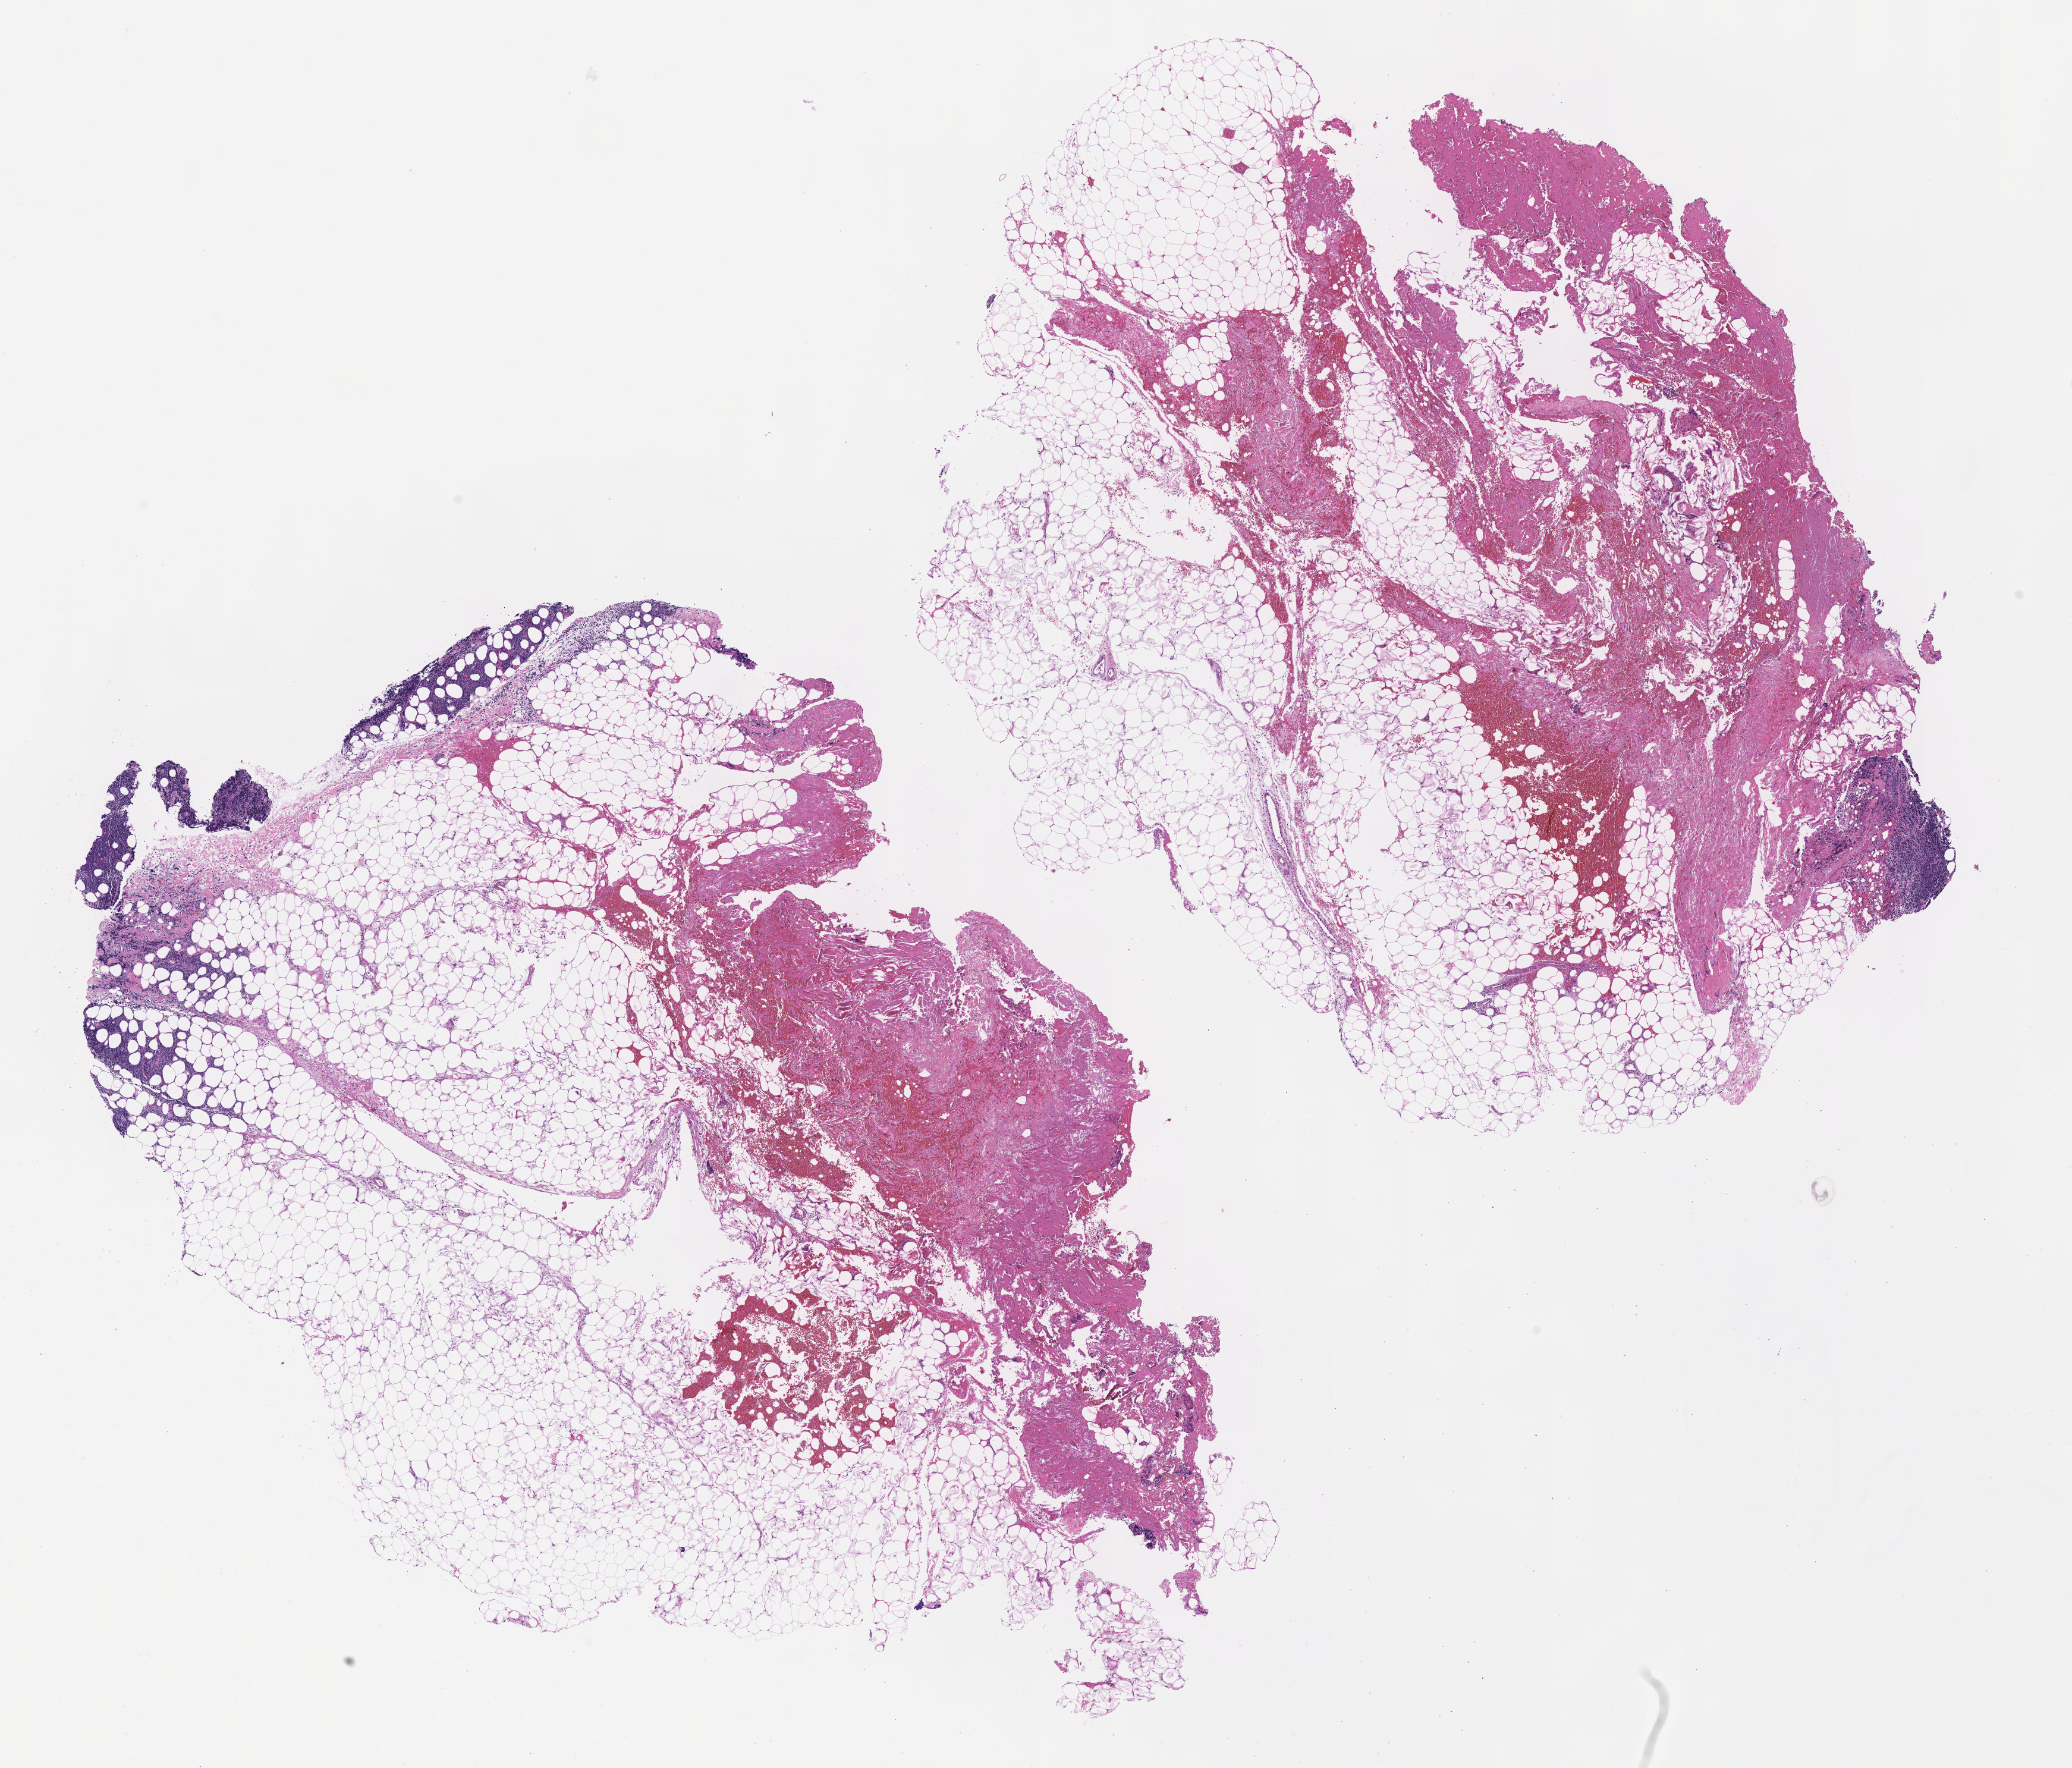
Haematoxylin and eosin whole-slide image — shown as a low-resolution overview of the whole scanned area (about 14.1 x 12.0 mm); tumor tissue; site: upper limb lymph node. Patient male; age 76 years.
Histologic diagnosis: Burkitt lymphoma, NOS.